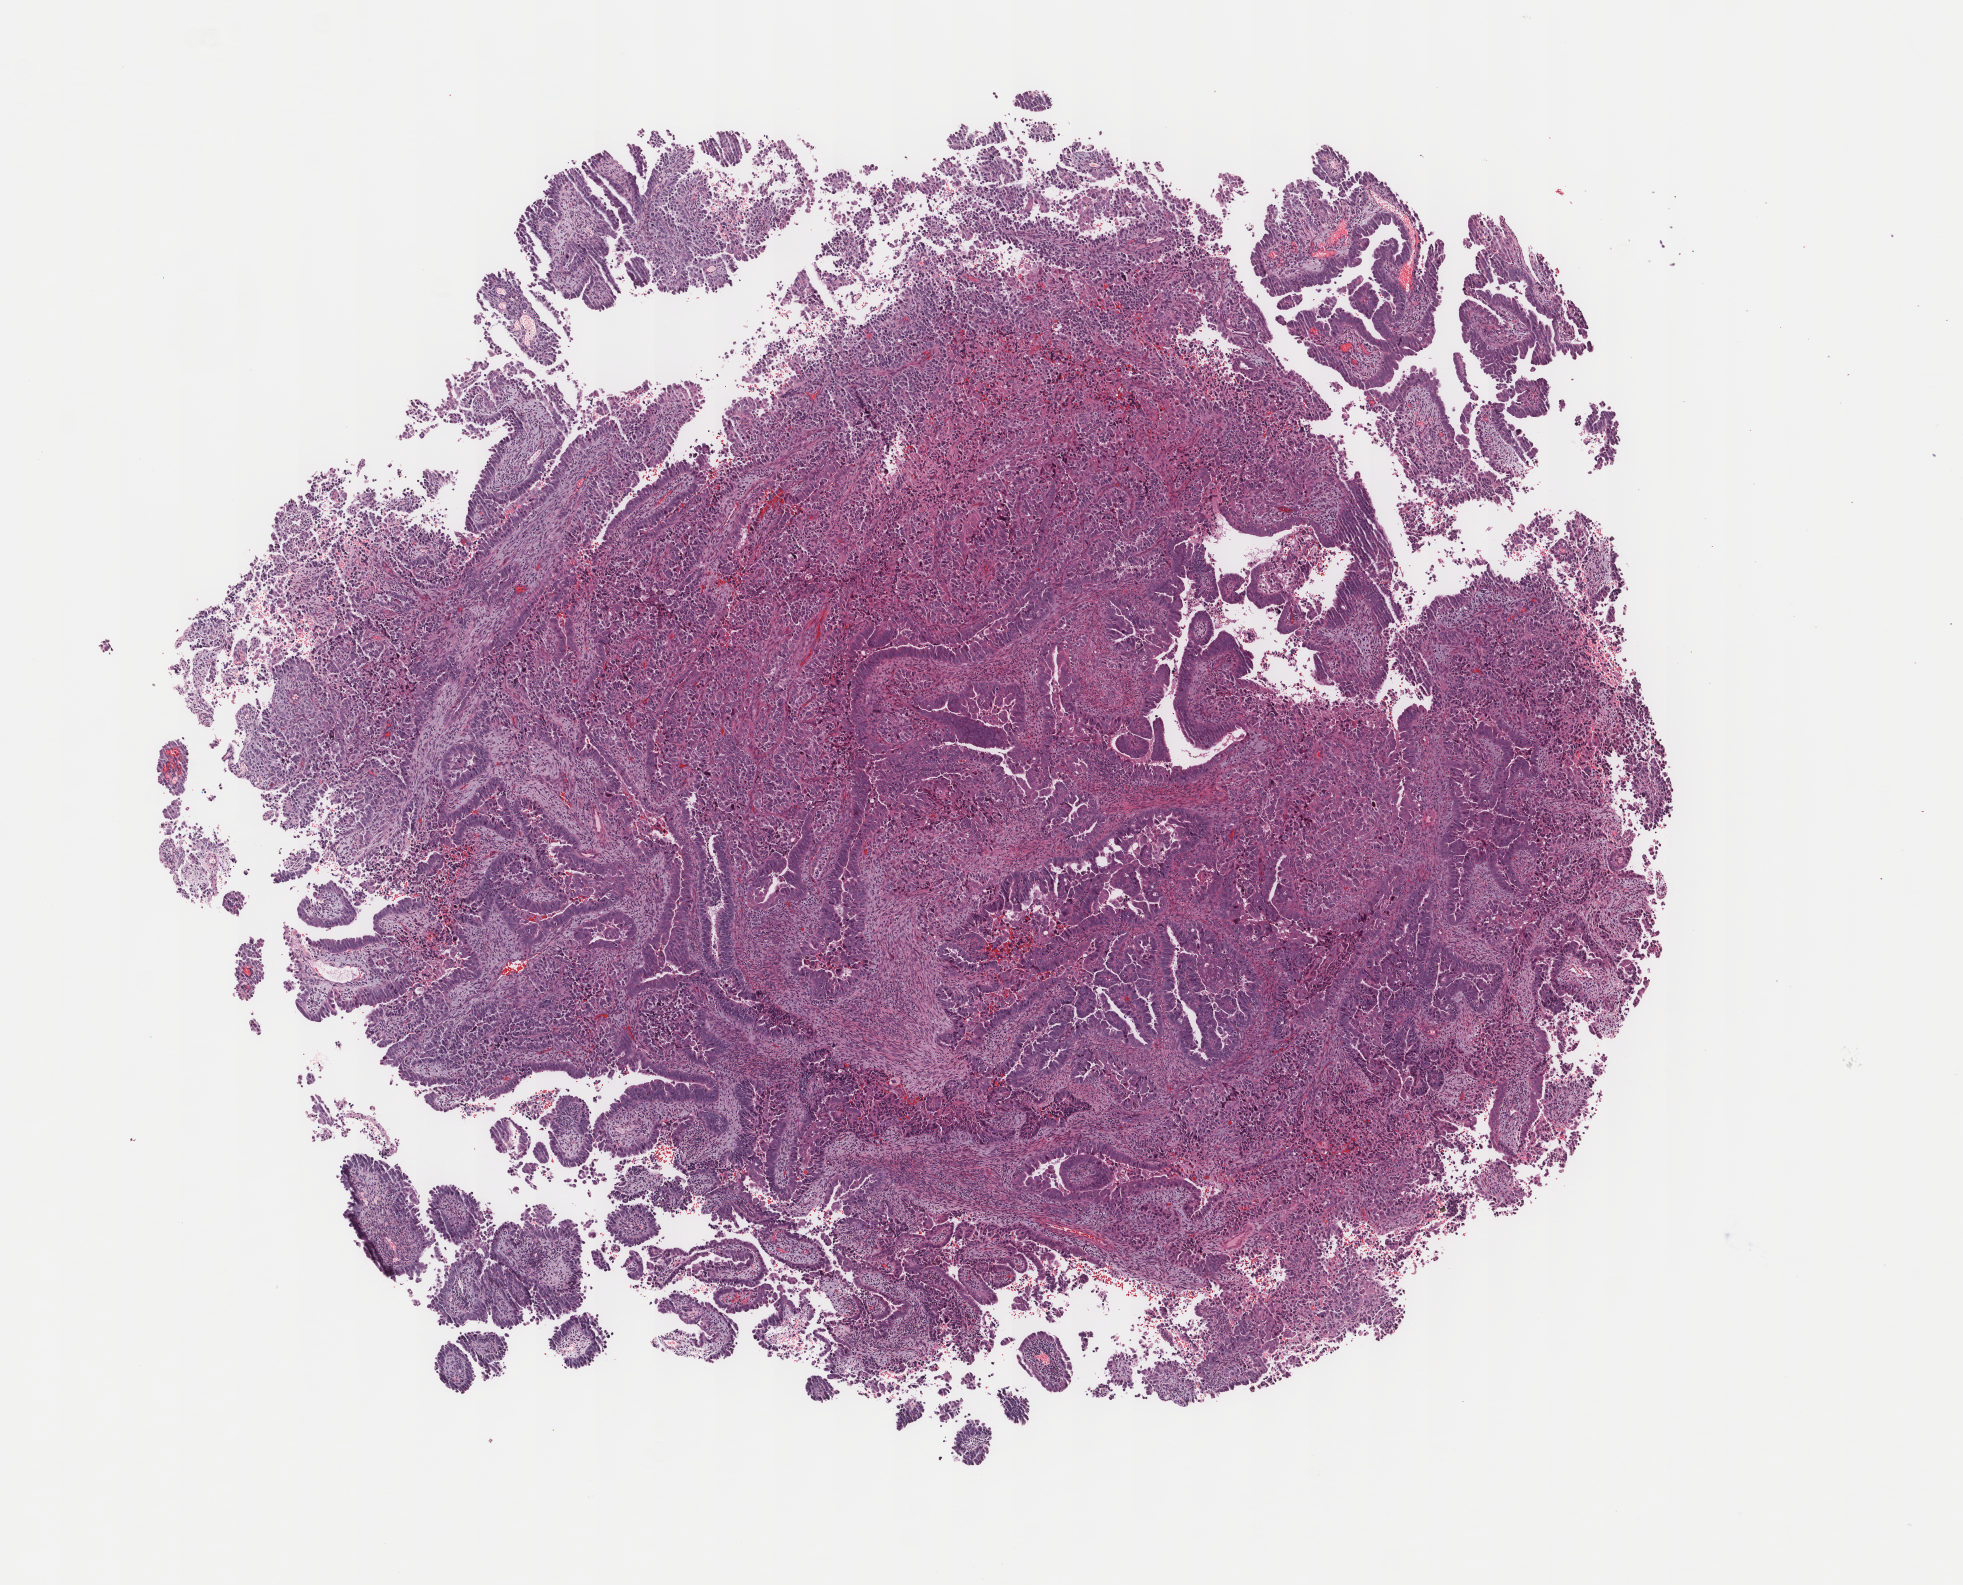
Whole-slide histology image, H&E — a low-resolution overview of the entire scanned area, about 7.8 x 6.3 mm, frozen section from the bottom of the tissue portion, uterus, primary tumour sample. Patient: female, age at initial diagnosis 71 years. Histologic grade: G3 (poorly differentiated). Pathologist review of this section (percent, as recorded): tumour cells 98%, tumour nuclei 75%, normal cells 0%, stromal cells 0%, necrosis 2%. Infiltration values recorded for this section: lymphocyte infiltration 4%, monocyte infiltration 0%, neutrophil infiltration 0%.
Pathologic diagnosis: Serous cystadenocarcinoma, NOS. FIGO stage: IIIC1.